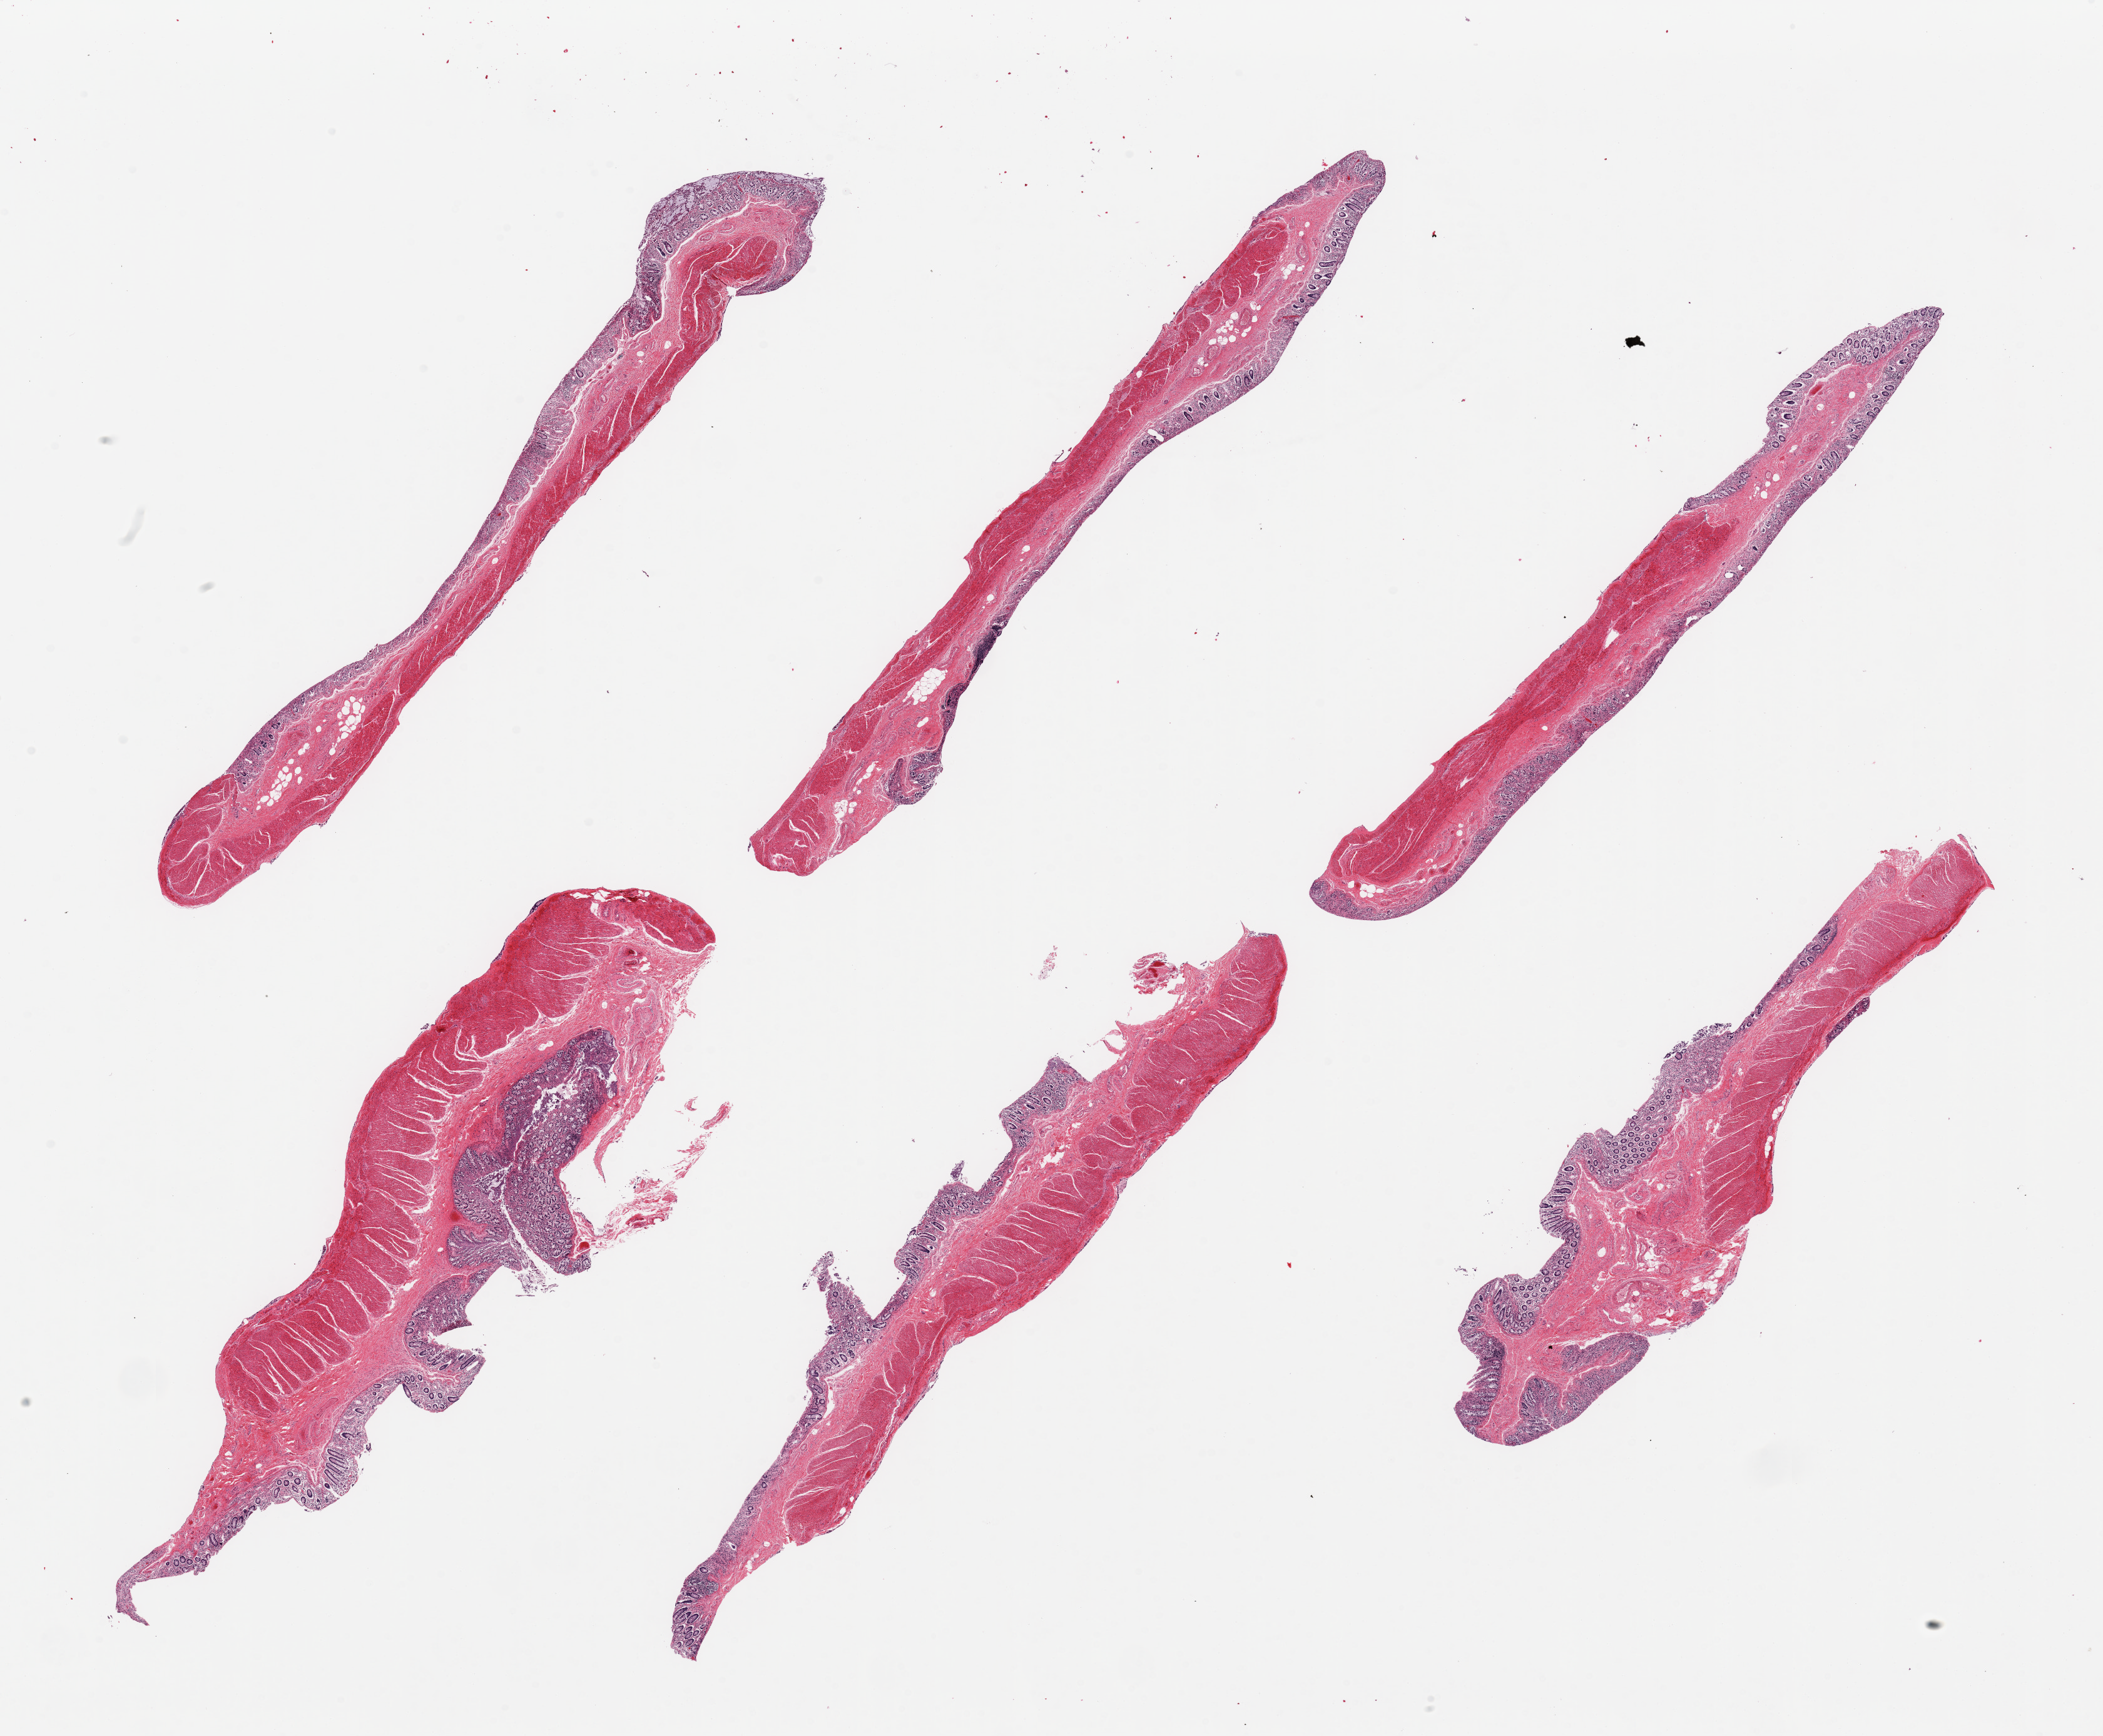
Digitized haematoxylin and eosin-stained section, brightfield — shown as a low-resolution overview of the whole scanned area (about 26.6 x 21.9 mm, acquisition: 20x scan), PAXgene-fixed, paraffin-embedded tissue, section of transverse colon (target tissue), donor tissue sample. Donor: male.
* review note (as recorded): 6 pieces, glandular mucoca with advanced autolysis, partially sloughing, up to ~0.4mm